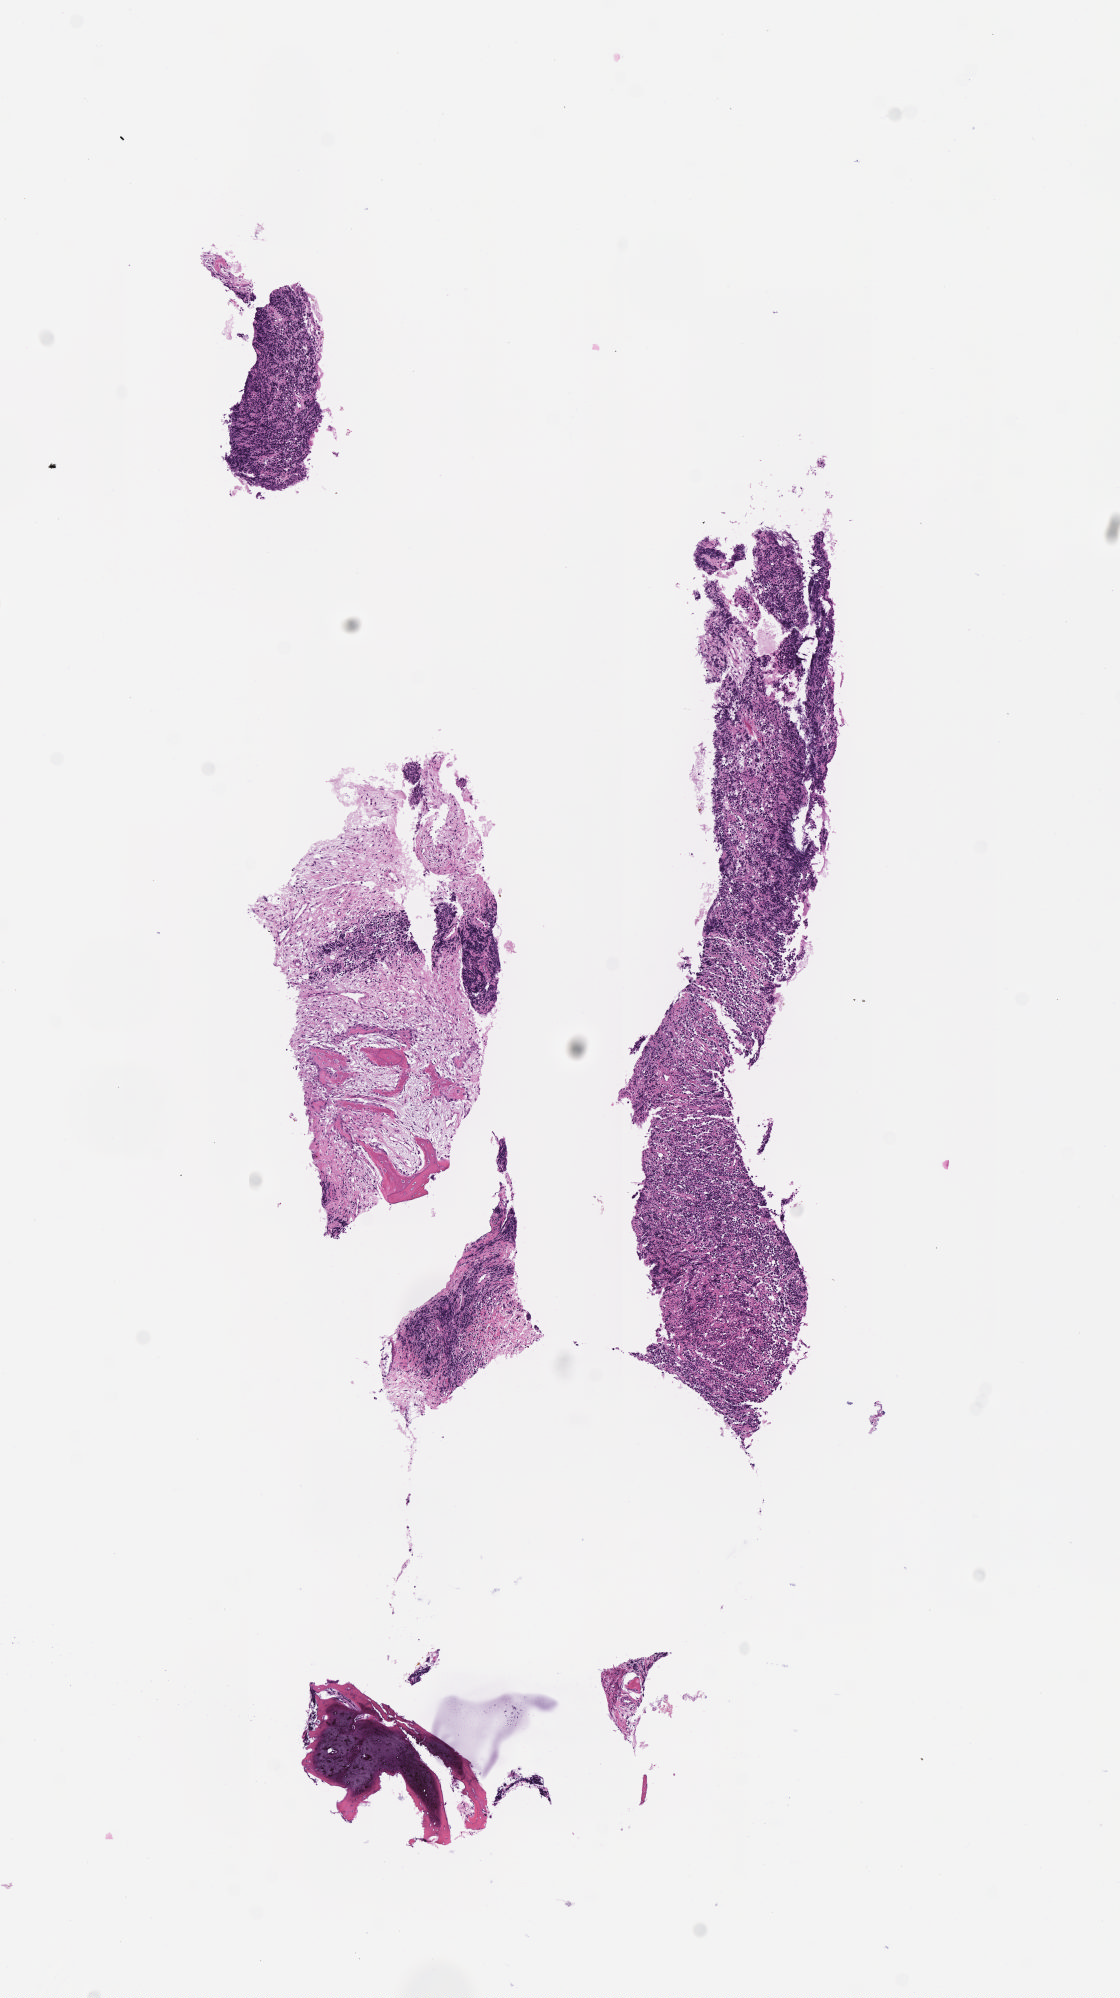
Digitized H&E-stained section, a low-resolution overview of the entire scanned area, about 4.5 x 8.1 mm. Tumor tissue. Anatomic site: mandible. Patient: male, age at initial diagnosis 6 years.
Histologic diagnosis: Burkitt lymphoma, NOS.